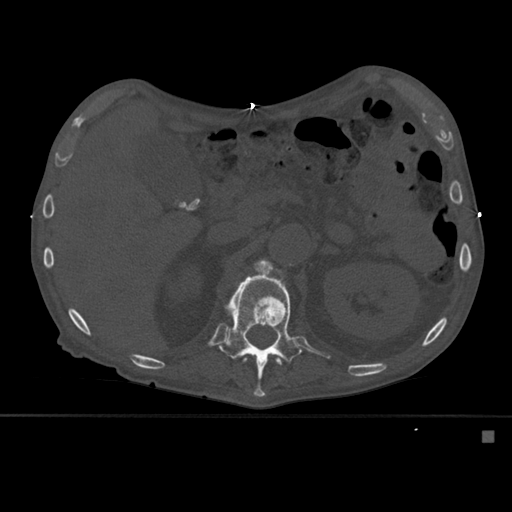
CT including the spine, one axial slice; slice 259 of 527 in the series (ordered by position); bone window (W 1800 / L 400 HU); 1.5 mm slice thickness; 512 × 512 image matrix, field of view 373 × 373 mm. Male patient, age 78 years. Case-level facts recorded for this patient, not image findings: primary cancer: prostate.
Annotated regions visible in this slice (semi-automatic segmentation, software-assisted and operator-edited):
- L1 vertebra: bounding box (x1, y1, x2, y2) in pixels: (220, 259, 302, 397)
- T12 vertebra: (242, 357, 282, 366)